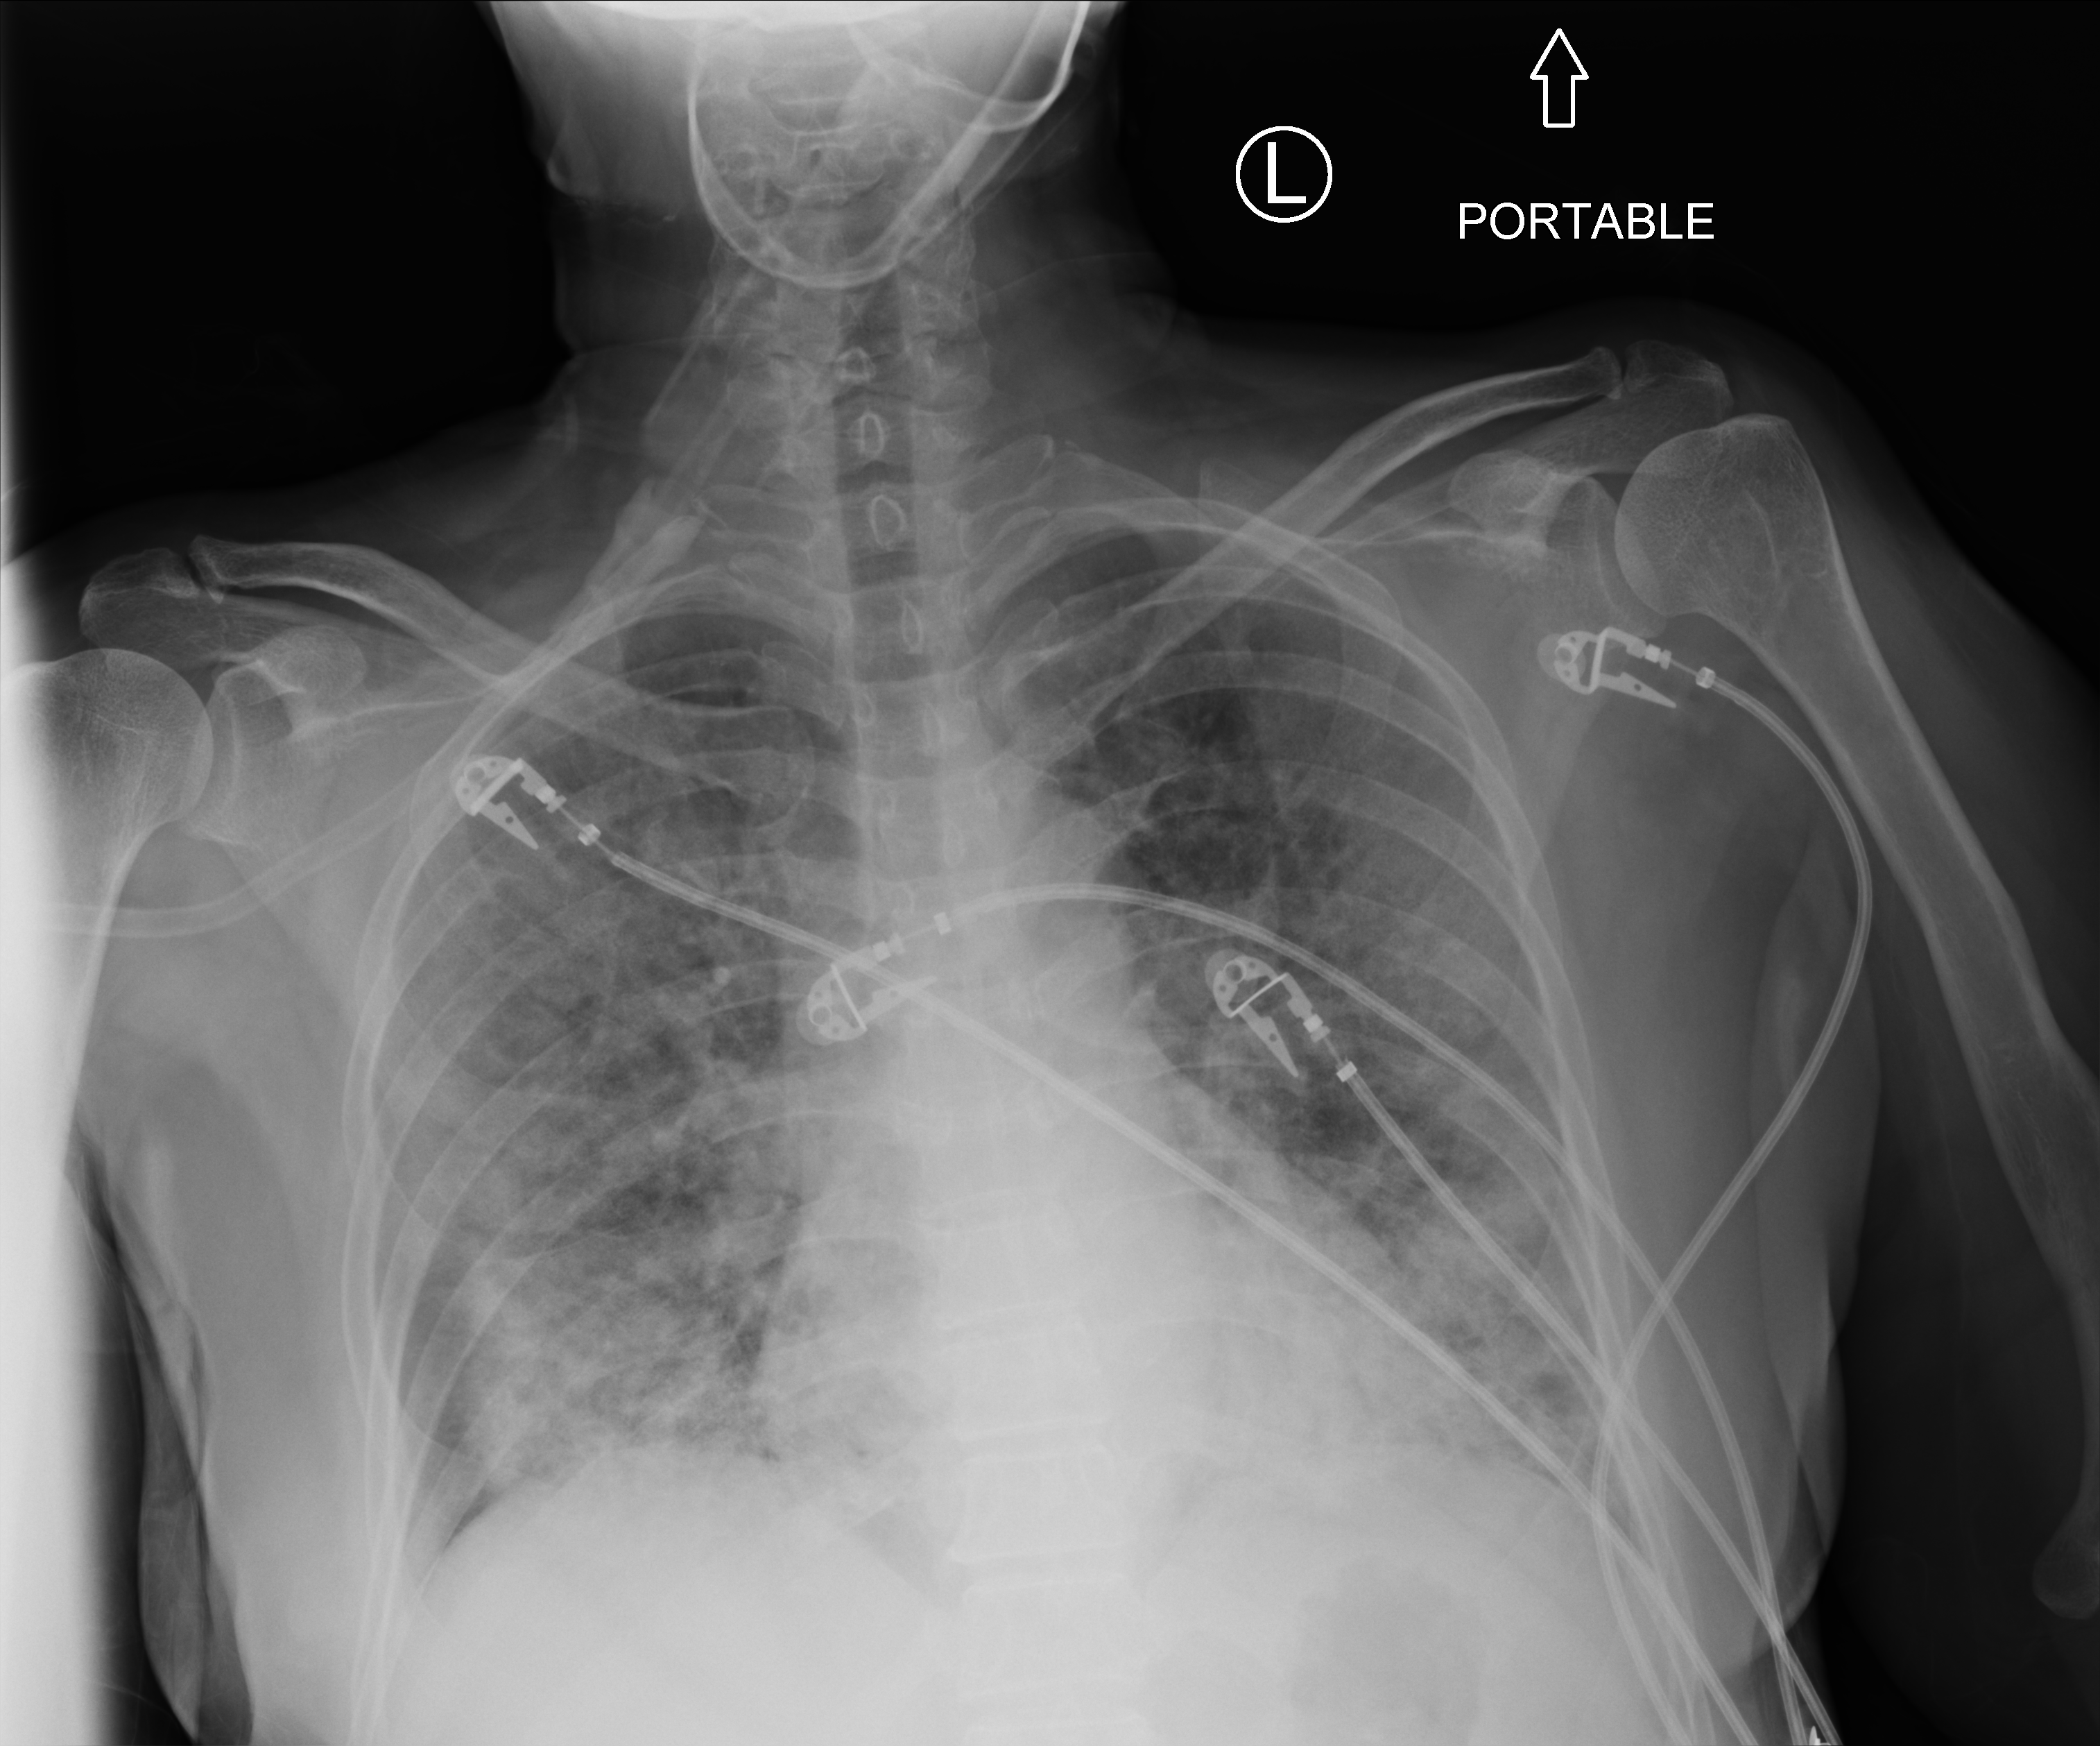
Bedside chest radiograph (computed radiography), anteroposterior (AP) projection. Female patient hospitalised with COVID-19, age 60–74 years.
Admission-level facts for this patient (not findings on this image; timing relative to this image not recorded): admitted to intensive care during this hospital stay: yes.